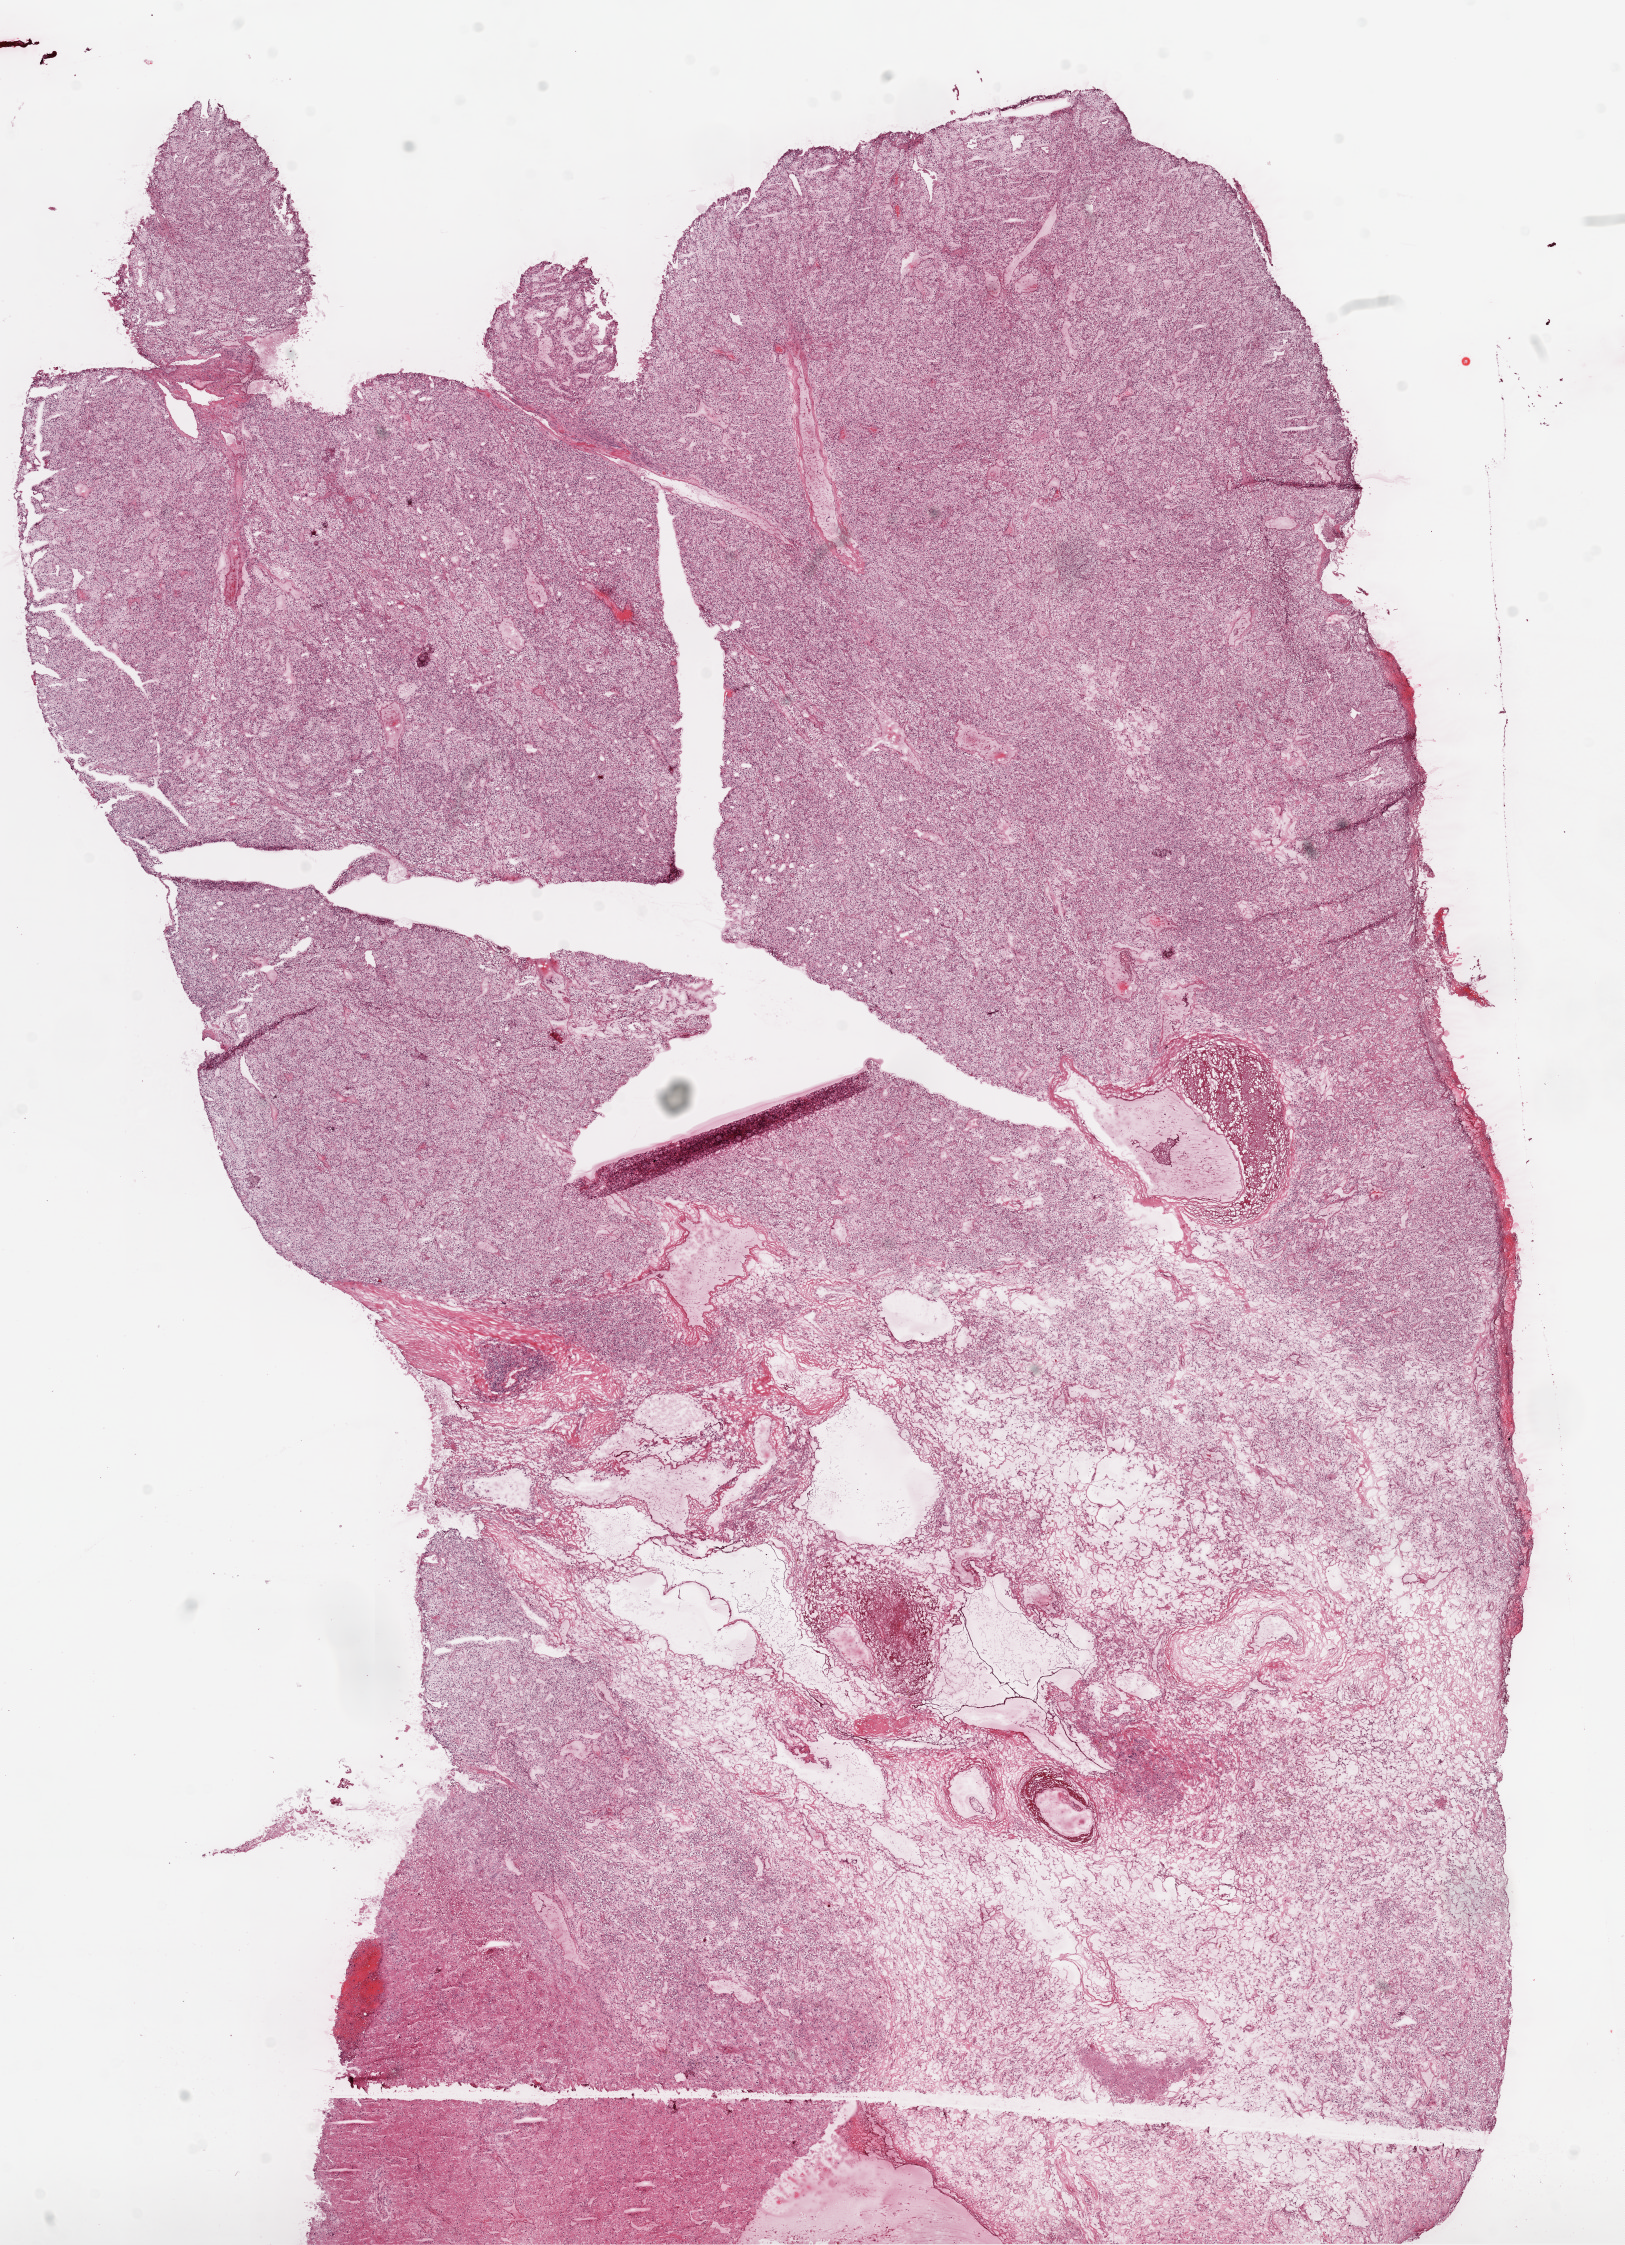
H&E whole-slide image — shown as a low-resolution overview of the whole scanned area (about 13.0 x 18.0 mm, slide scanned at 20x); frozen section from the top of the tissue portion; sample: primary tumour, kidney. Female, age 75 years at initial diagnosis. Histologic grade: G2 (moderately differentiated). Pathologist review of this section (percent, as recorded): tumour cells 90%, tumour nuclei 90%, normal cells 0%, stromal cells 10%, necrosis 0%.
• pathologic diagnosis: Clear cell adenocarcinoma, NOS
• laterality: right
• AJCC pathologic stage: II
• lymph nodes positive (case pathology): 0 of 6 examined
• TNM: T2 N0 M0